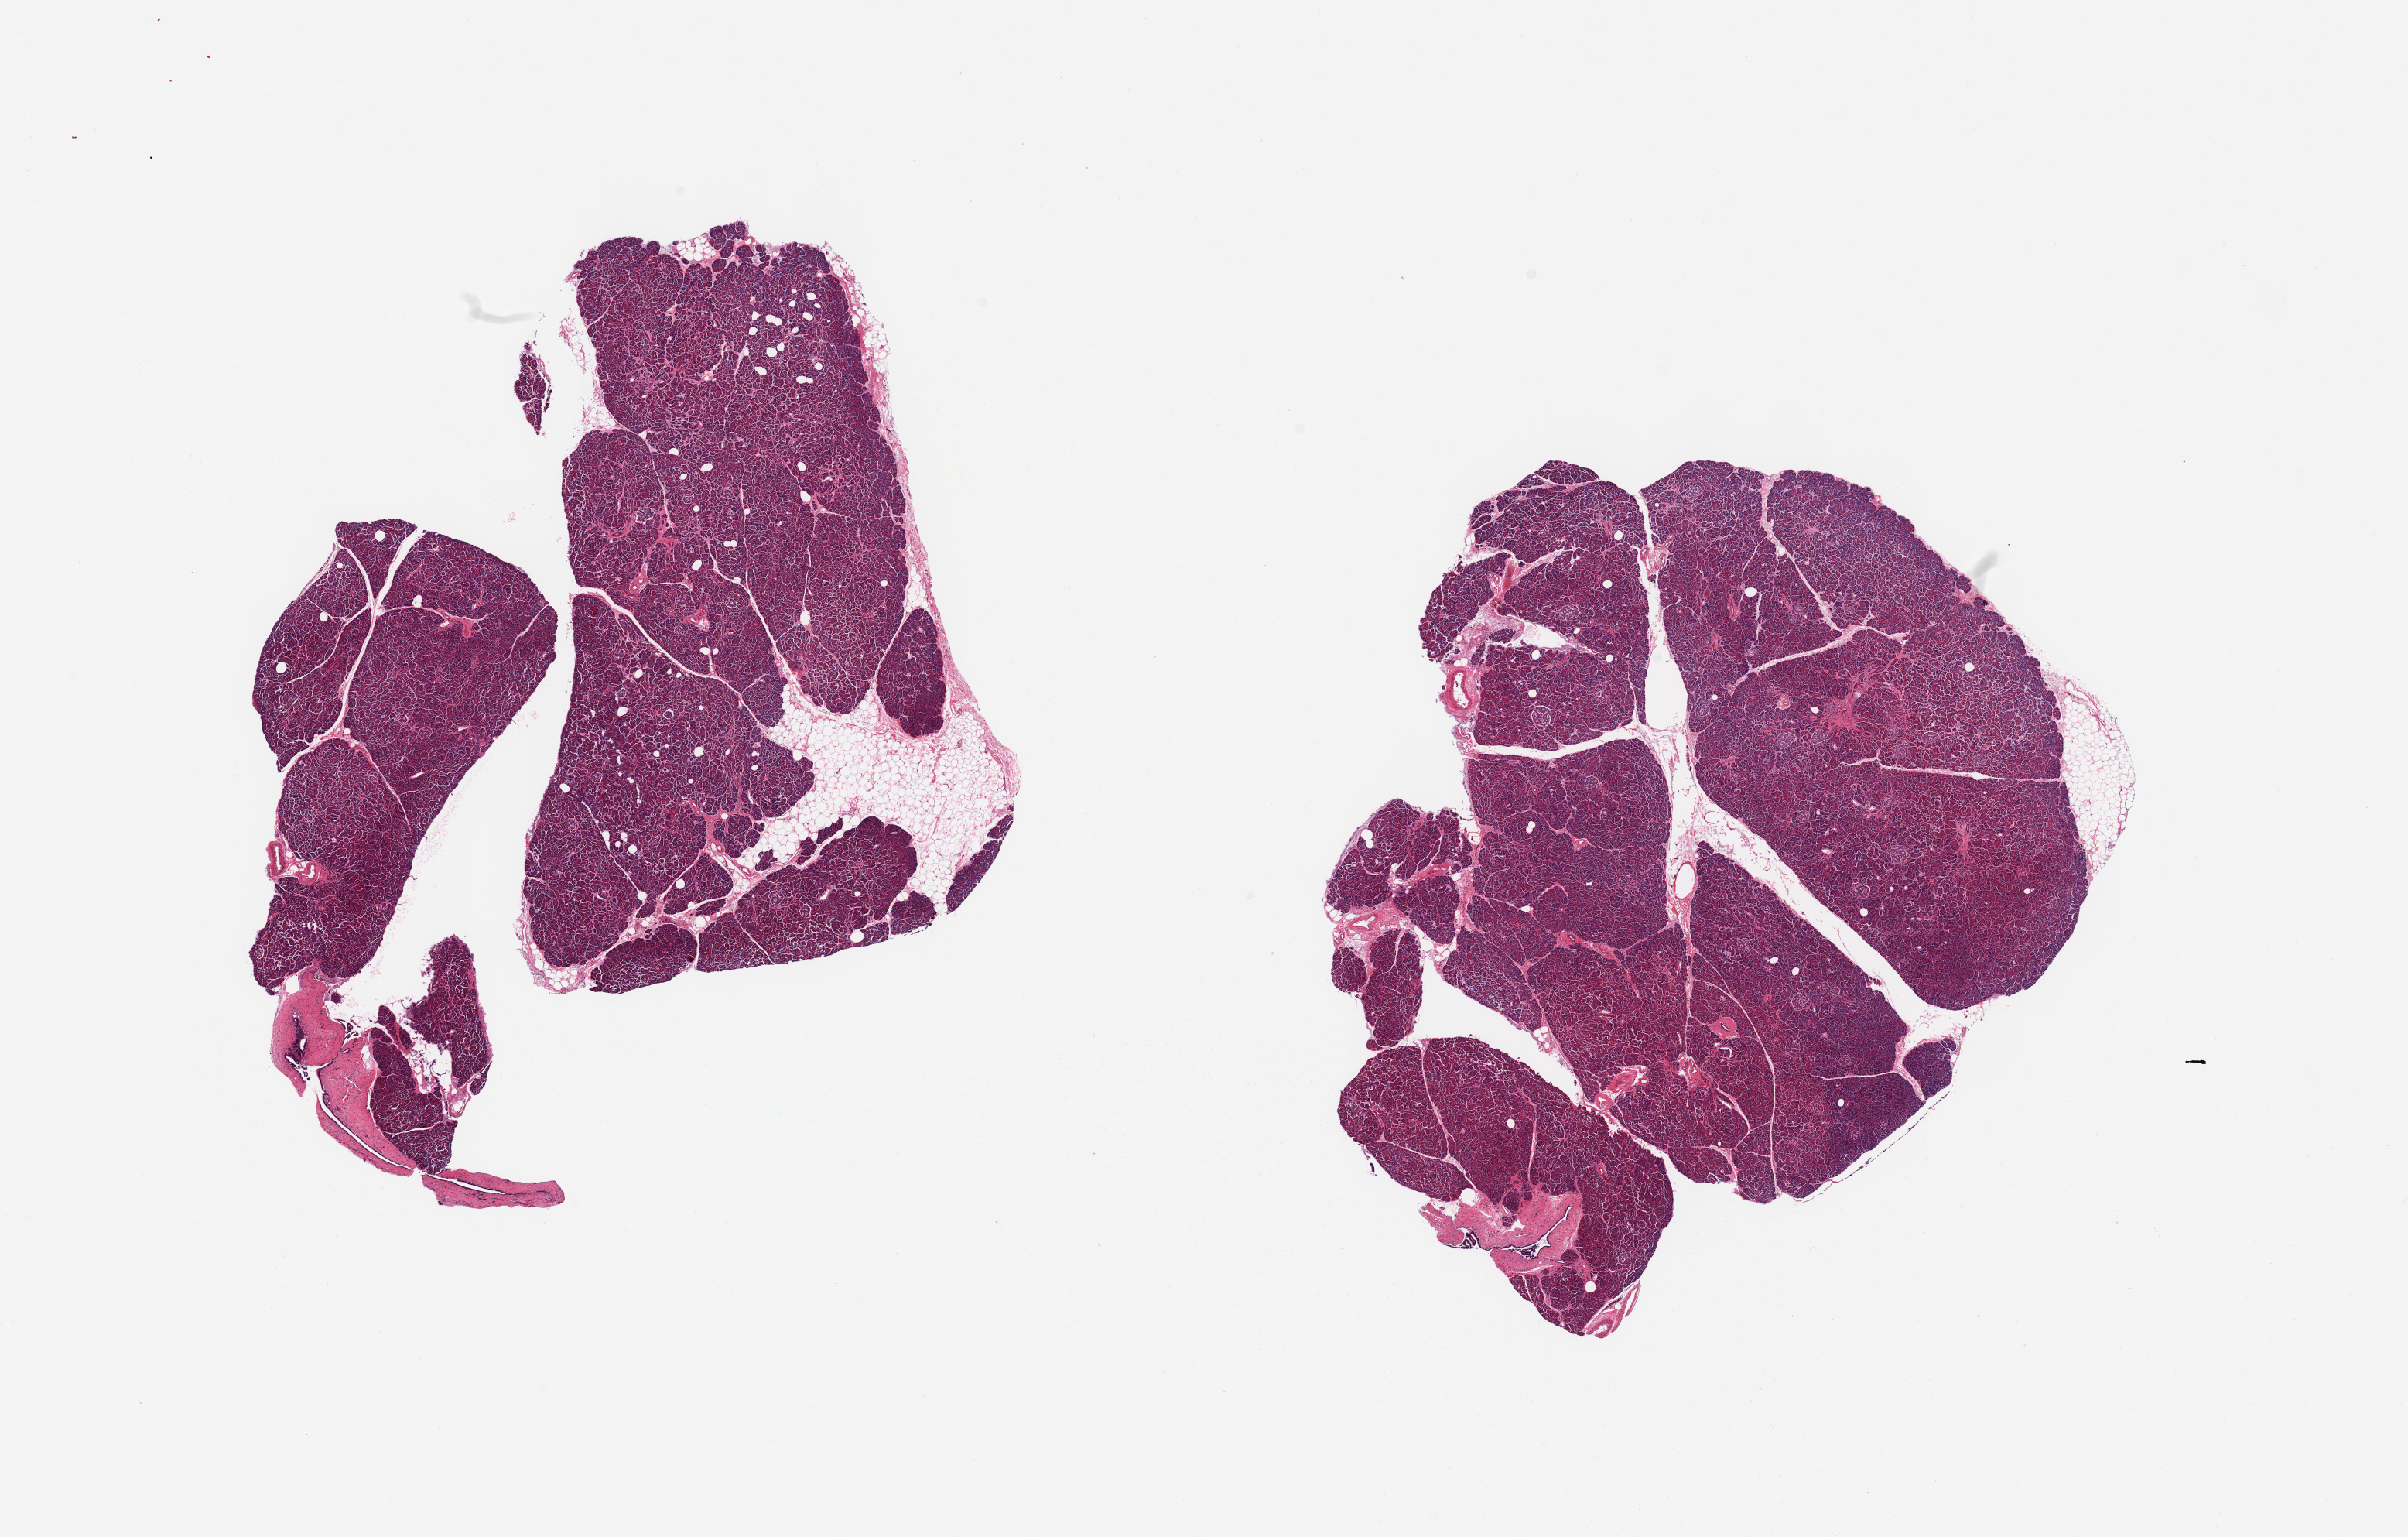
Digitized haematoxylin and eosin-stained section — a low-resolution overview of the entire scanned area, about 24.6 x 15.7 mm (slide scanned at 20x); PAXgene-fixed paraffin-embedded (PFPE) section; section of pancreas (target tissue); tissue donor sample.
Review note (as recorded): 2 pieces, mild saponification; islets well- preserved, moderate numbers.